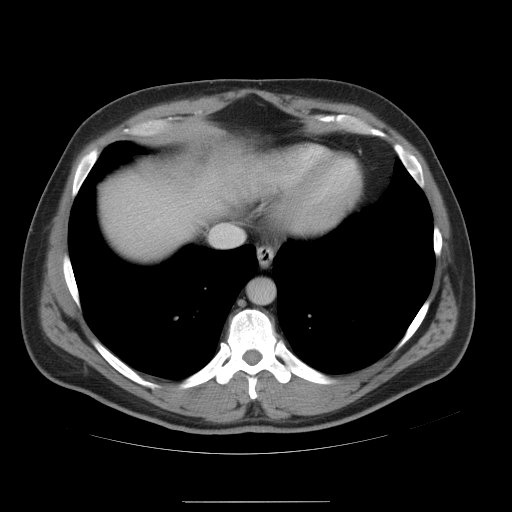
Contrast-enhanced abdominal CT, one axial slice; slice 47 of 54 in the series (ordered by position); 120 kVp; intravenous contrast given; soft-tissue window (W 400 / L 40 HU); 5 mm slice thickness; 512 × 512 image matrix. Male patient, age 40 years. Case-level facts recorded for this patient, not image findings: diagnosis: colorectal cancer liver metastases, imaged before liver resection; multiple liver metastases: no; largest metastasis: 15 cm; disease in both lobes: no.
Outlined on this slice (outlined manually by an expert reader):
- hepatic veins: bounding box (x1, y1, x2, y2) in pixels: (213, 226, 242, 246)
- liver: (98, 138, 276, 263)
- planned liver remnant (the part of the liver to remain after resection): (176, 137, 277, 226)